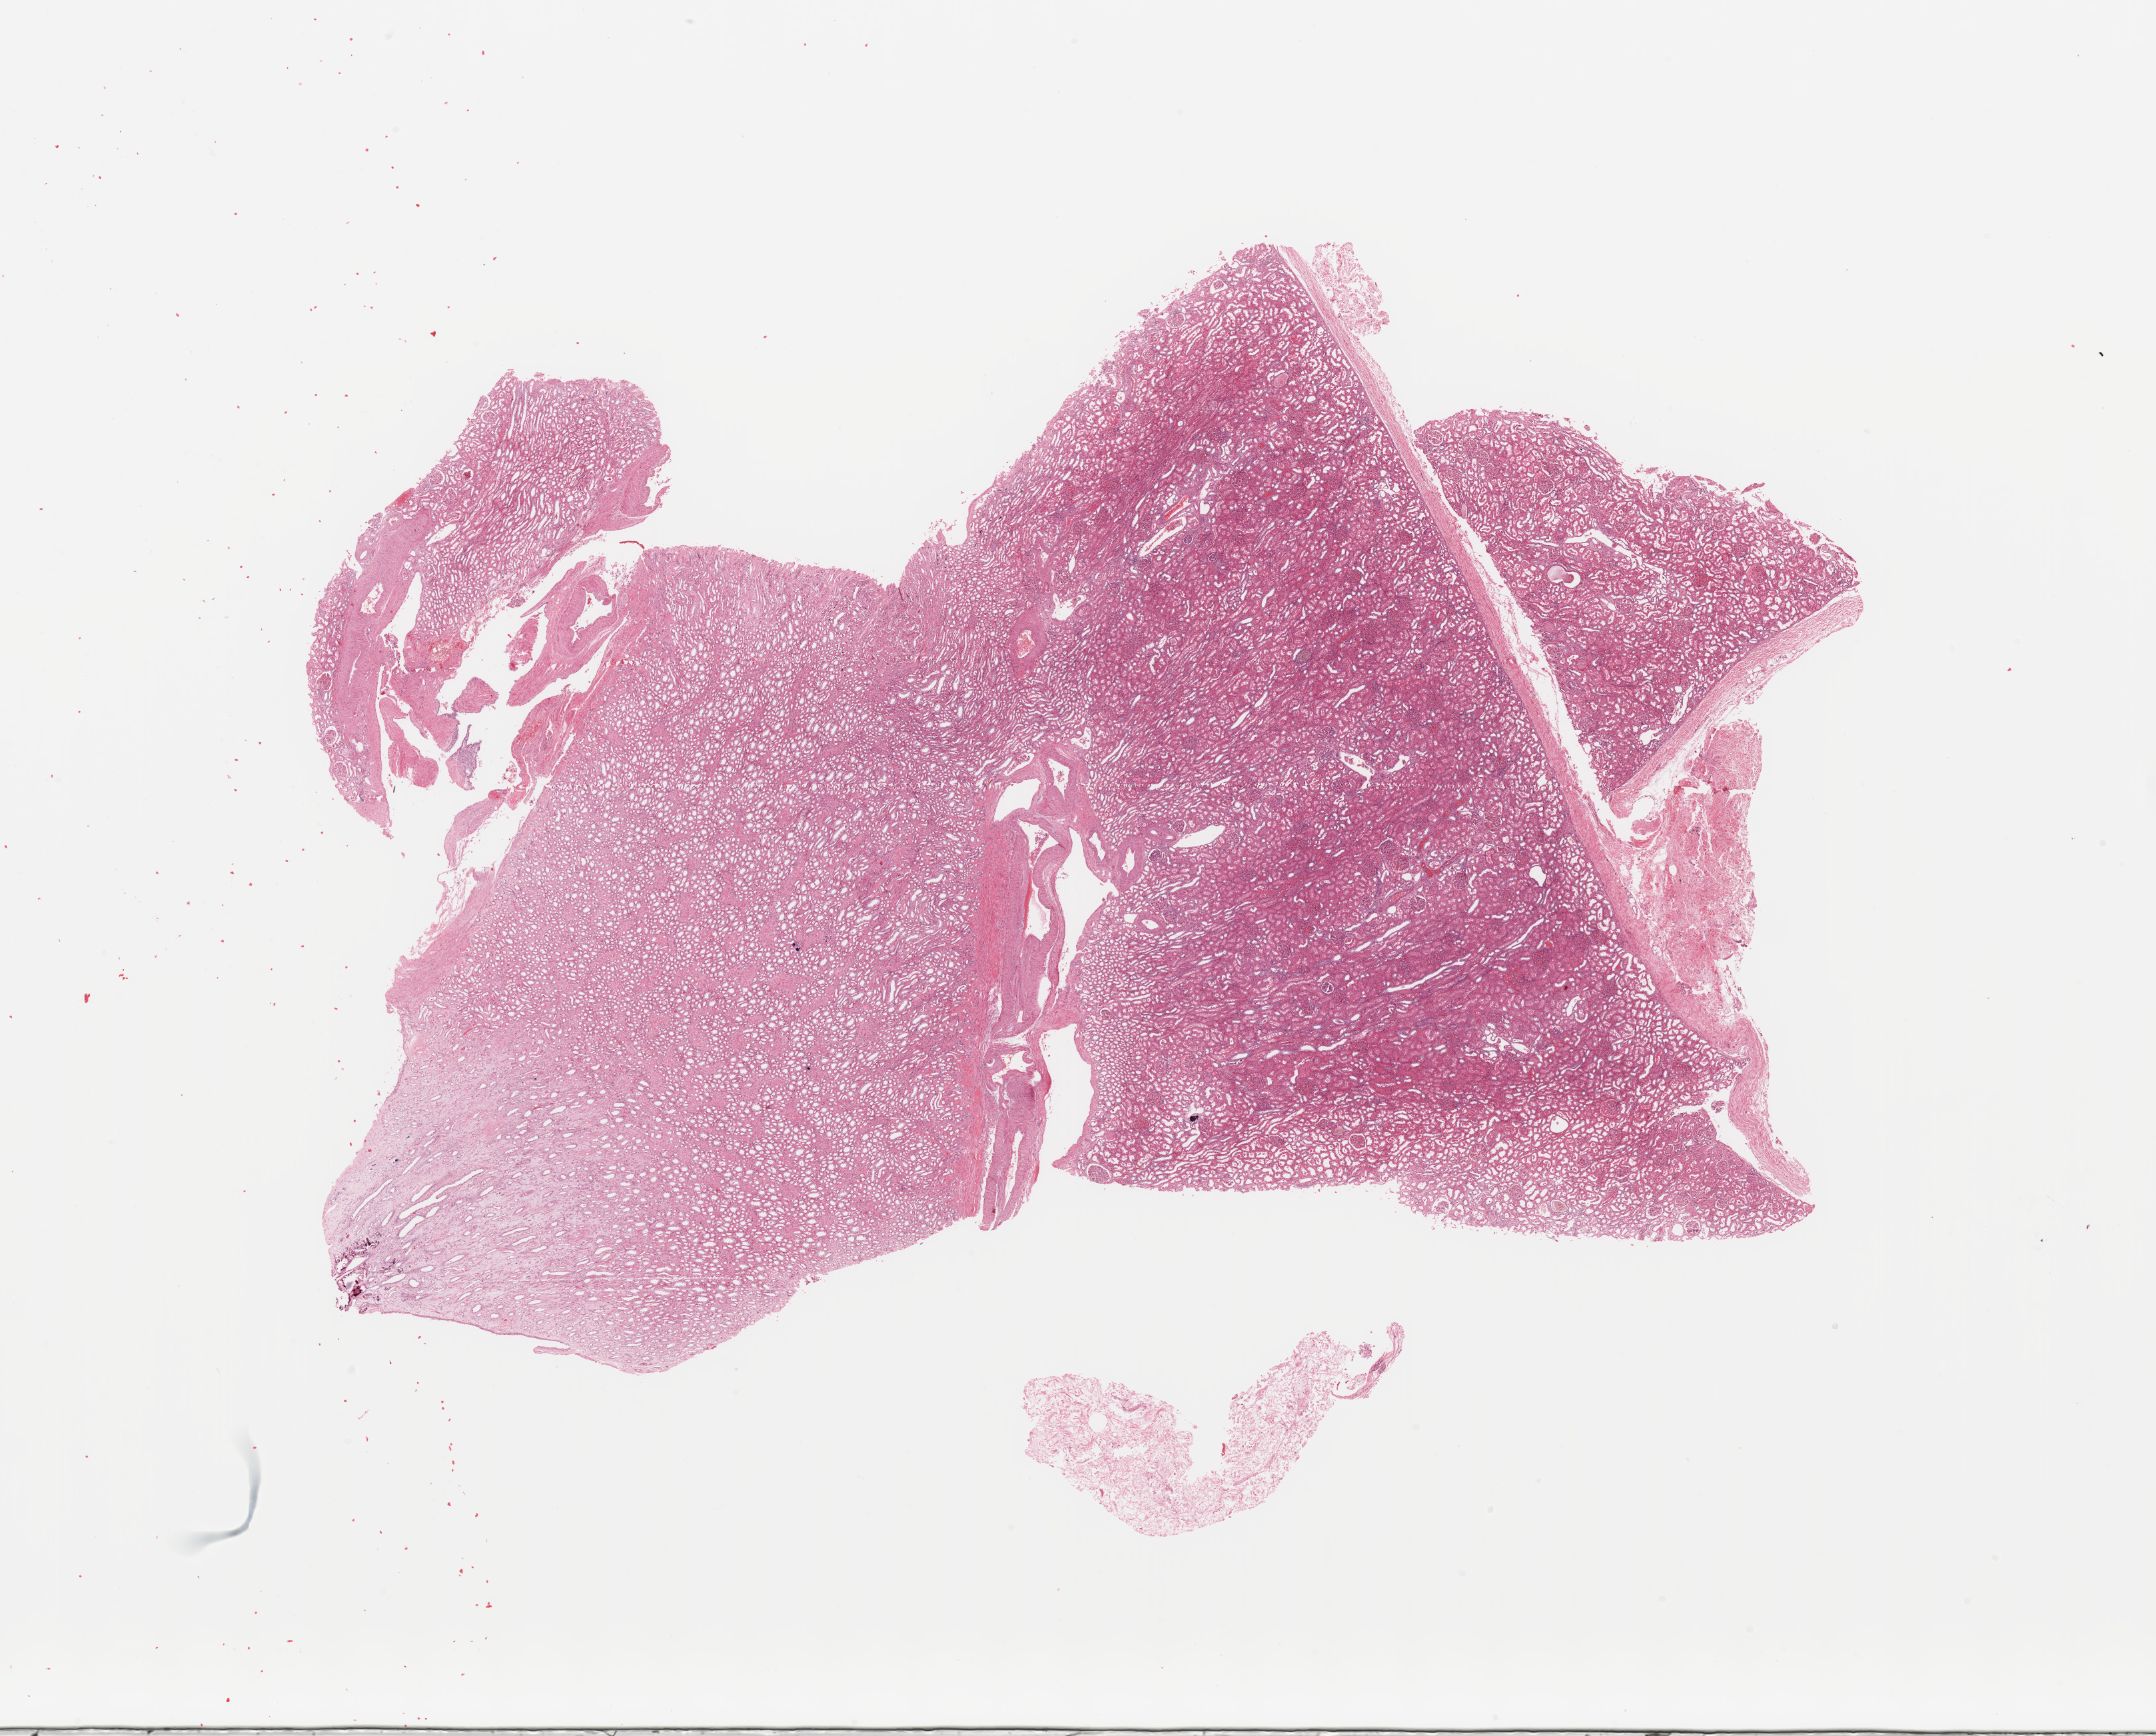
Whole-slide histology image, Hematoxylin and eosin (H&E) stained — shown as a low-resolution overview of the whole scanned area (about 25.6 x 20.6 mm, from a 20x scan), normal (non-tumour) tissue sample, kidney. 54-year-old female patient.
* this section: normal (non-tumour) tissue from the same patient
* patient diagnosis: Renal cell carcinoma, NOS